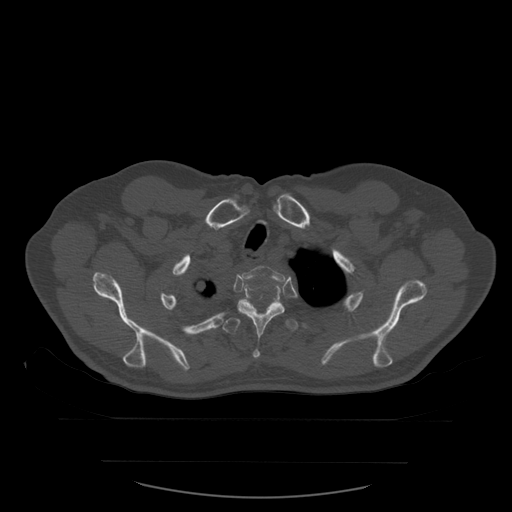
CT including the spine, one axial slice; position 457 of 590 along the scan axis; bone window (W 1800 / L 400 HU); 1.25 mm slice thickness; 512 × 512 image matrix, field of view 479 × 479 mm. Patient age 71 years. From the clinical record (not read from this slice): primary cancer: lung.
Outlined on this slice (semi-automatically segmented with operator editing):
- T2 vertebra: bounding box (x1, y1, x2, y2) in pixels: (243, 266, 285, 282)
- T3 vertebra: (237, 286, 285, 359)
- T4 vertebra: (223, 299, 299, 334)